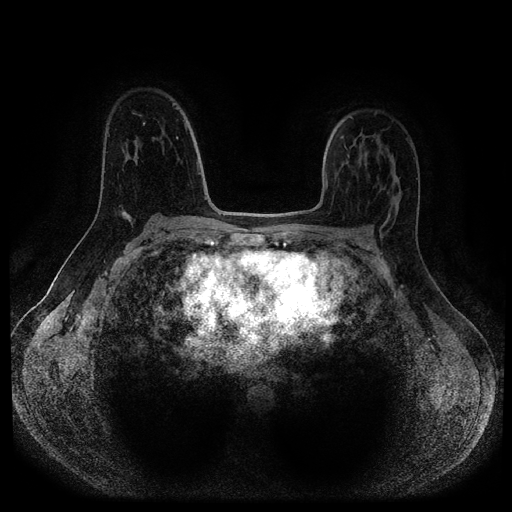
Breast MRI (dynamic contrast-enhanced, multi-phase), one axial slice. Slice 68 of 116 in the series (ordered by position). Dynamic contrast-enhanced series, time point 2 of 5 at this slice position (early post-contrast). 1.5 T. TE 2.7 ms, TR 5.4 ms. 2 mm slice thickness. 512 × 512 image matrix. Female patient, age 40 years.
Annotated regions visible in this slice (semi-automatic segmentation, software-assisted and operator-edited):
- breast lesion (labelled benign in the annotation): box from (x=119, y=208) to (x=135, y=228) px